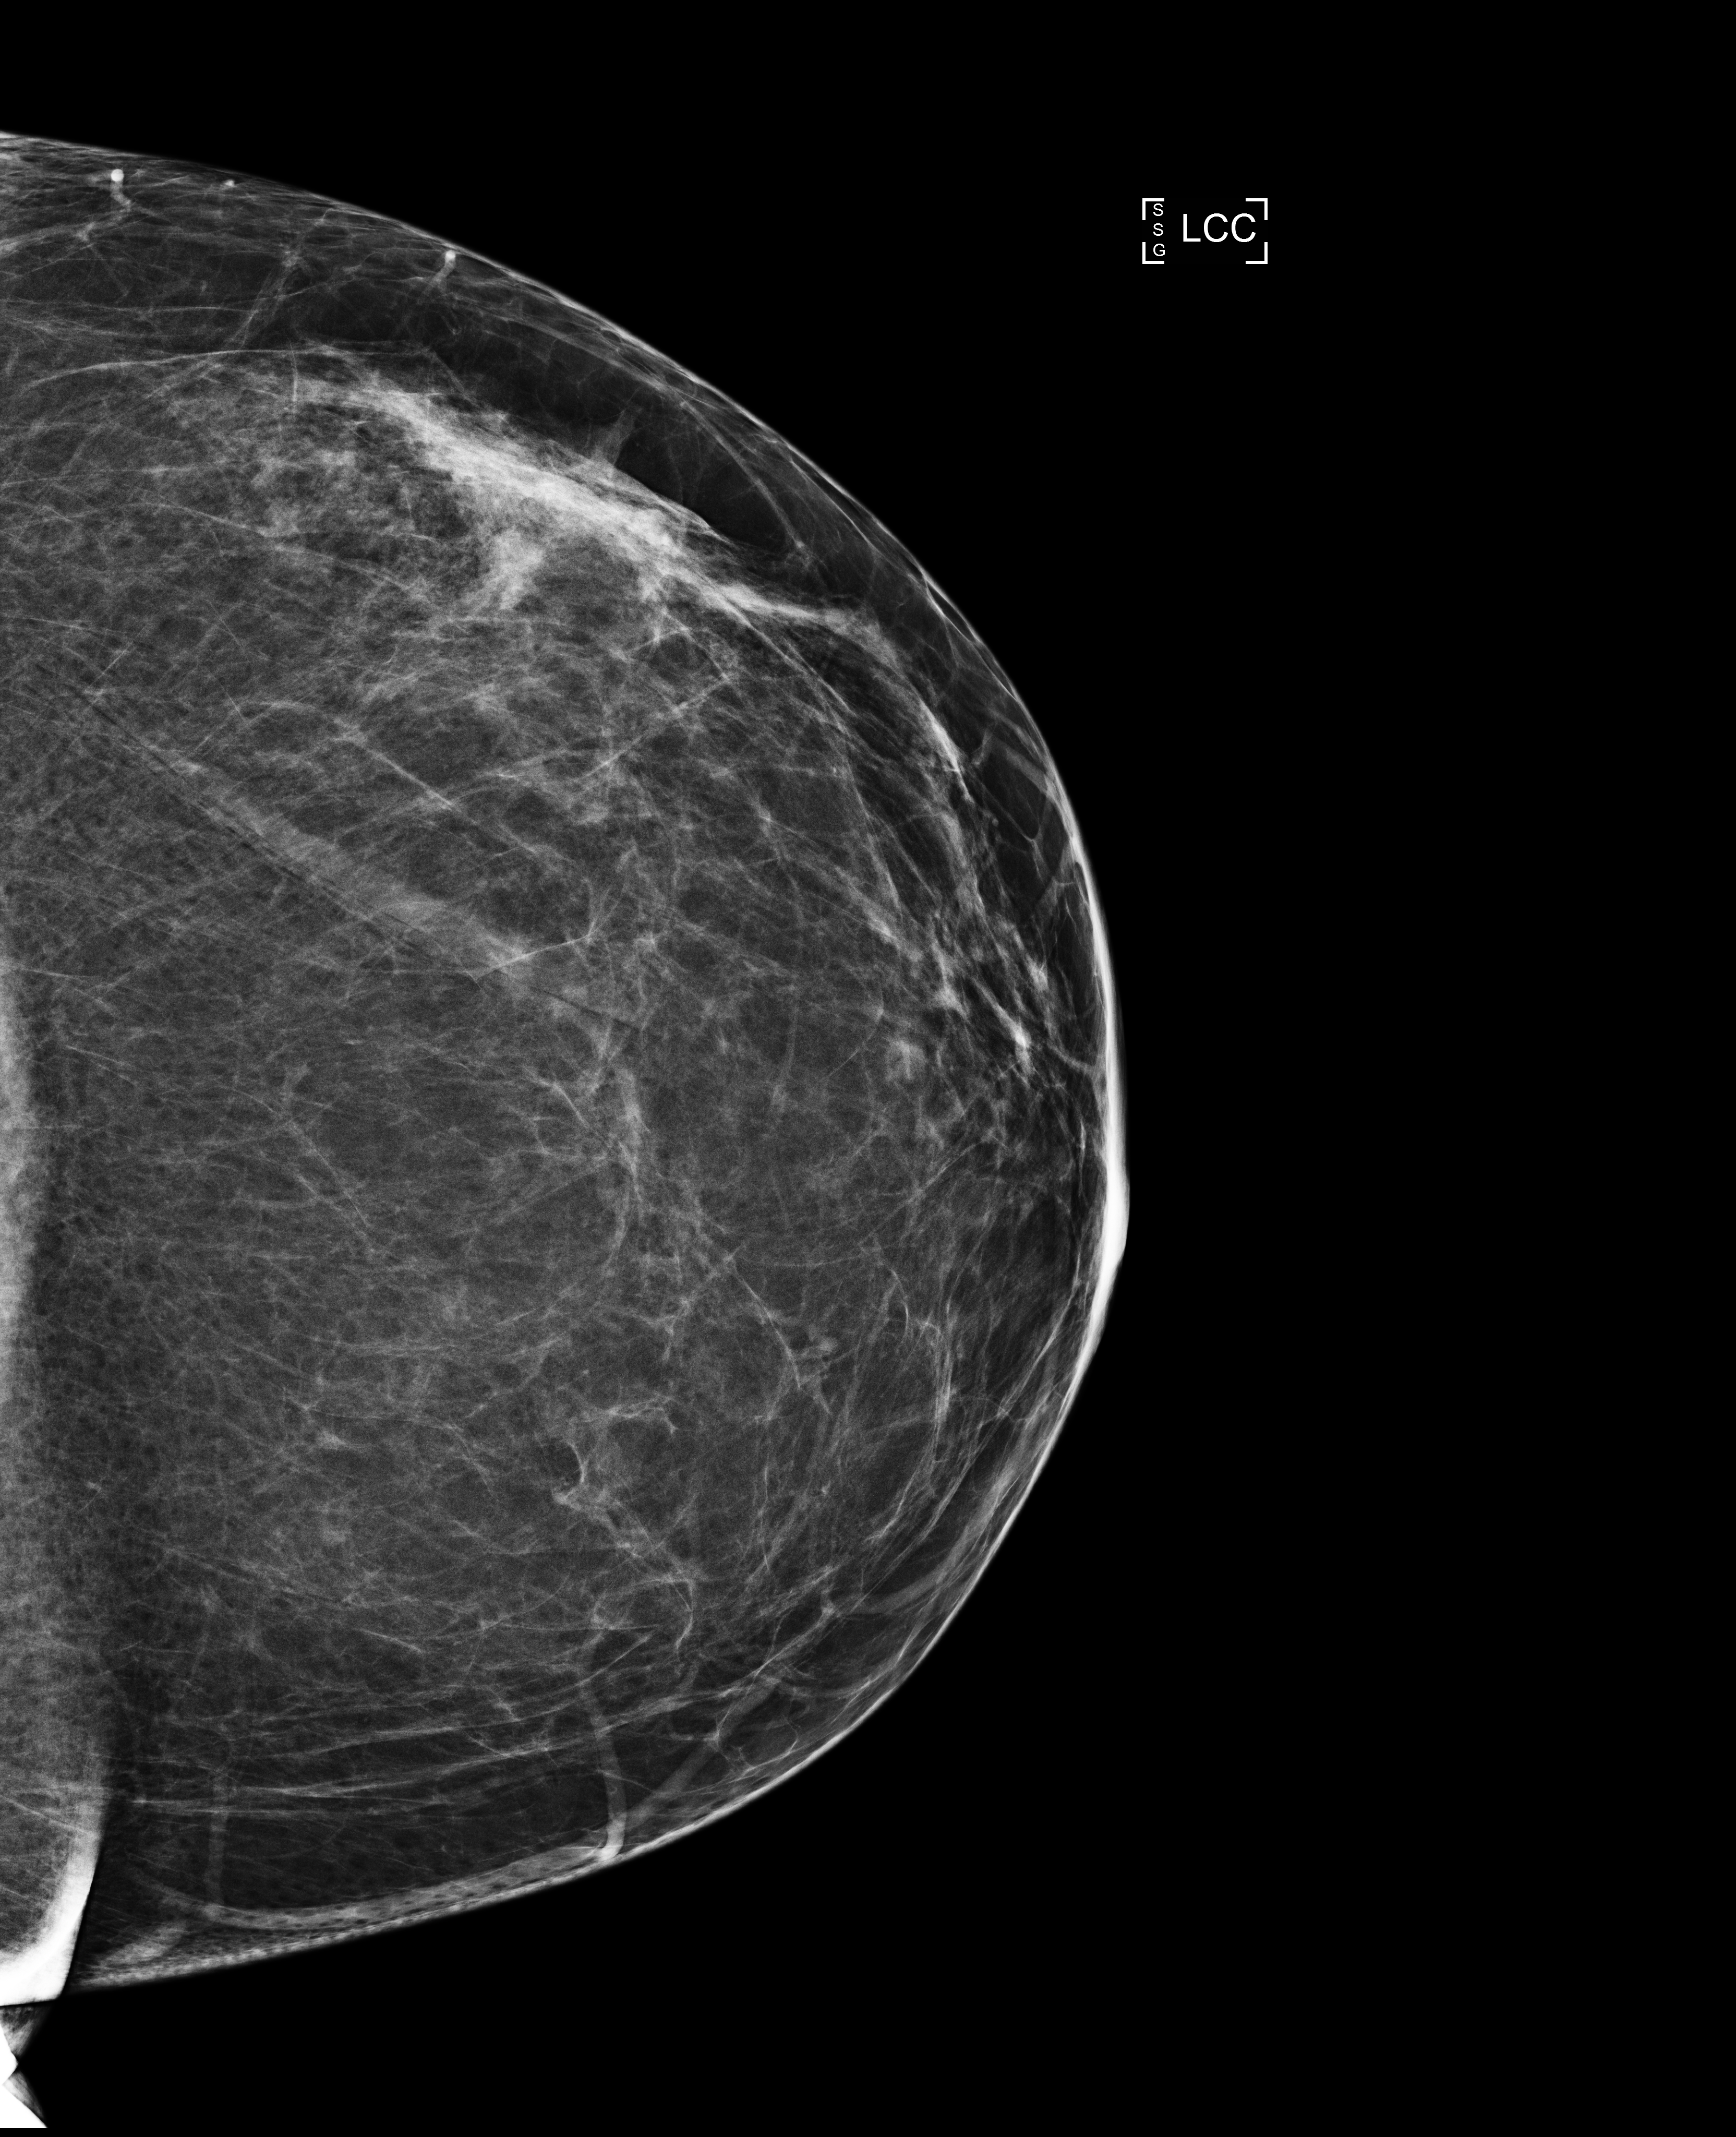
Screening examination, compressed breast thickness 71 mm. Patient: female, 51 years.
Image type: full-field digital mammogram. Breast: left. Projection: CC view. BI-RADS breast density category at the screening exam (both breasts, scale 1–4): 2. Final BI-RADS assessment for this screening round (tomosynthesis exam, both breasts): category 2. Recall: no recall after this screen.